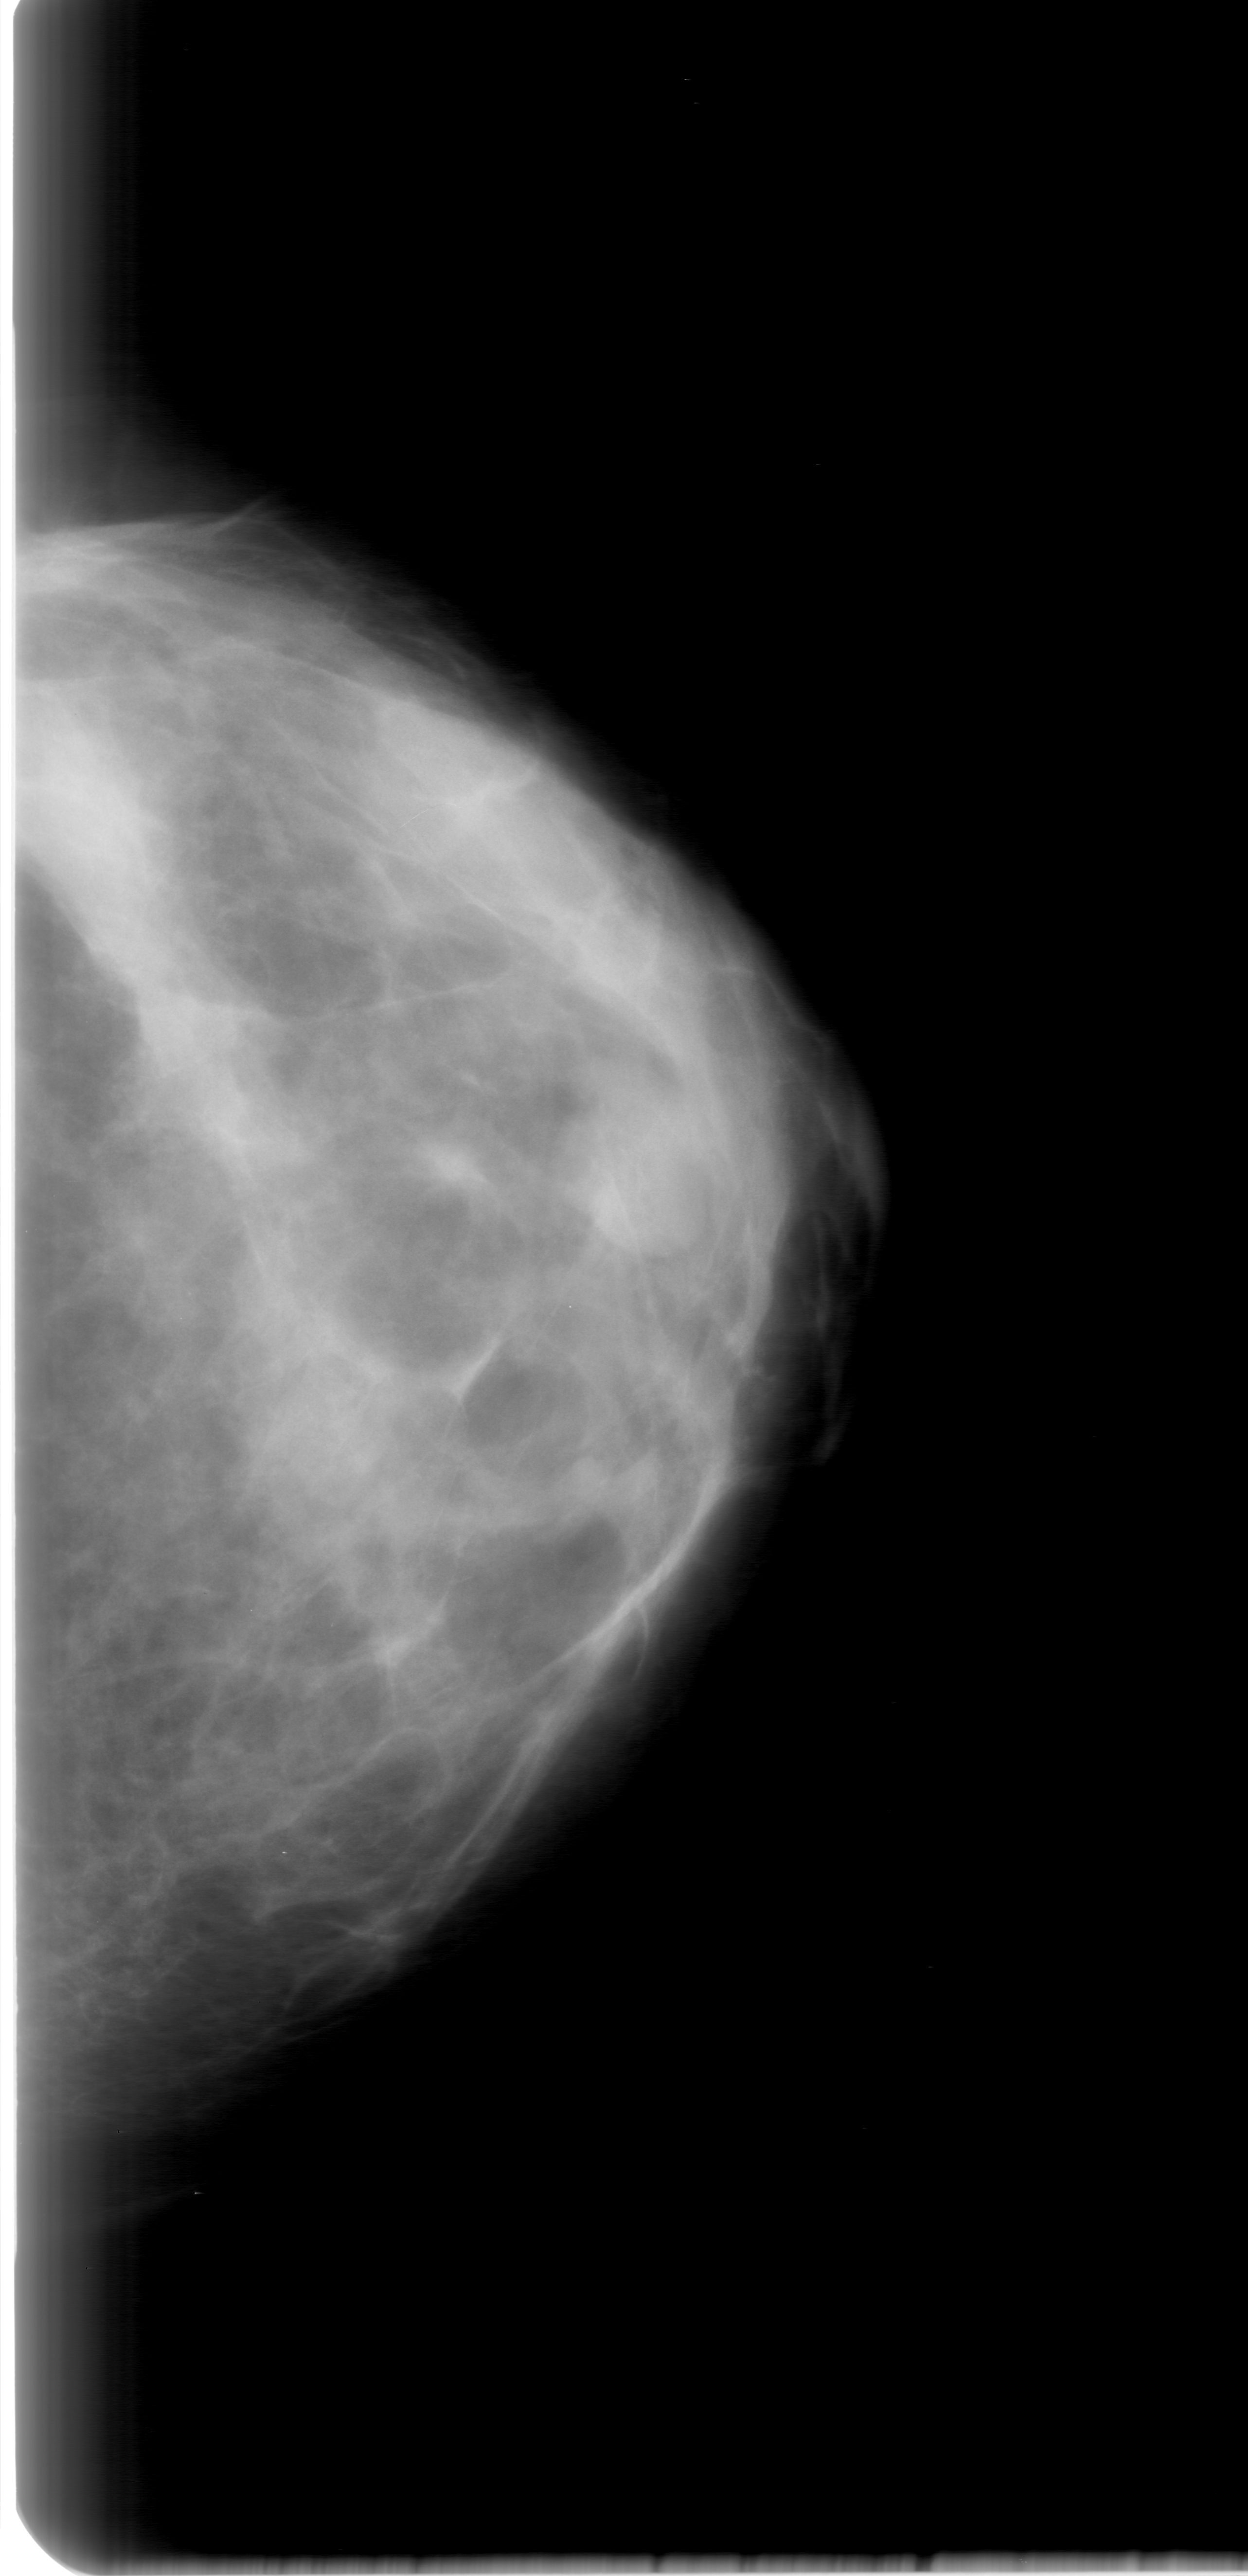
Scanned film-screen mammogram; left breast; craniocaudal (CC) view; breast composition: heterogeneously dense (BI-RADS density category 3 of 4).
Marked abnormality: mass, shape lobulated, margins circumscribed; BI-RADS assessment category 0 (incomplete: needs additional imaging); subtlety rating 4 on a 1 (subtle) to 5 (obvious) scale; pathology (as recorded): benign.